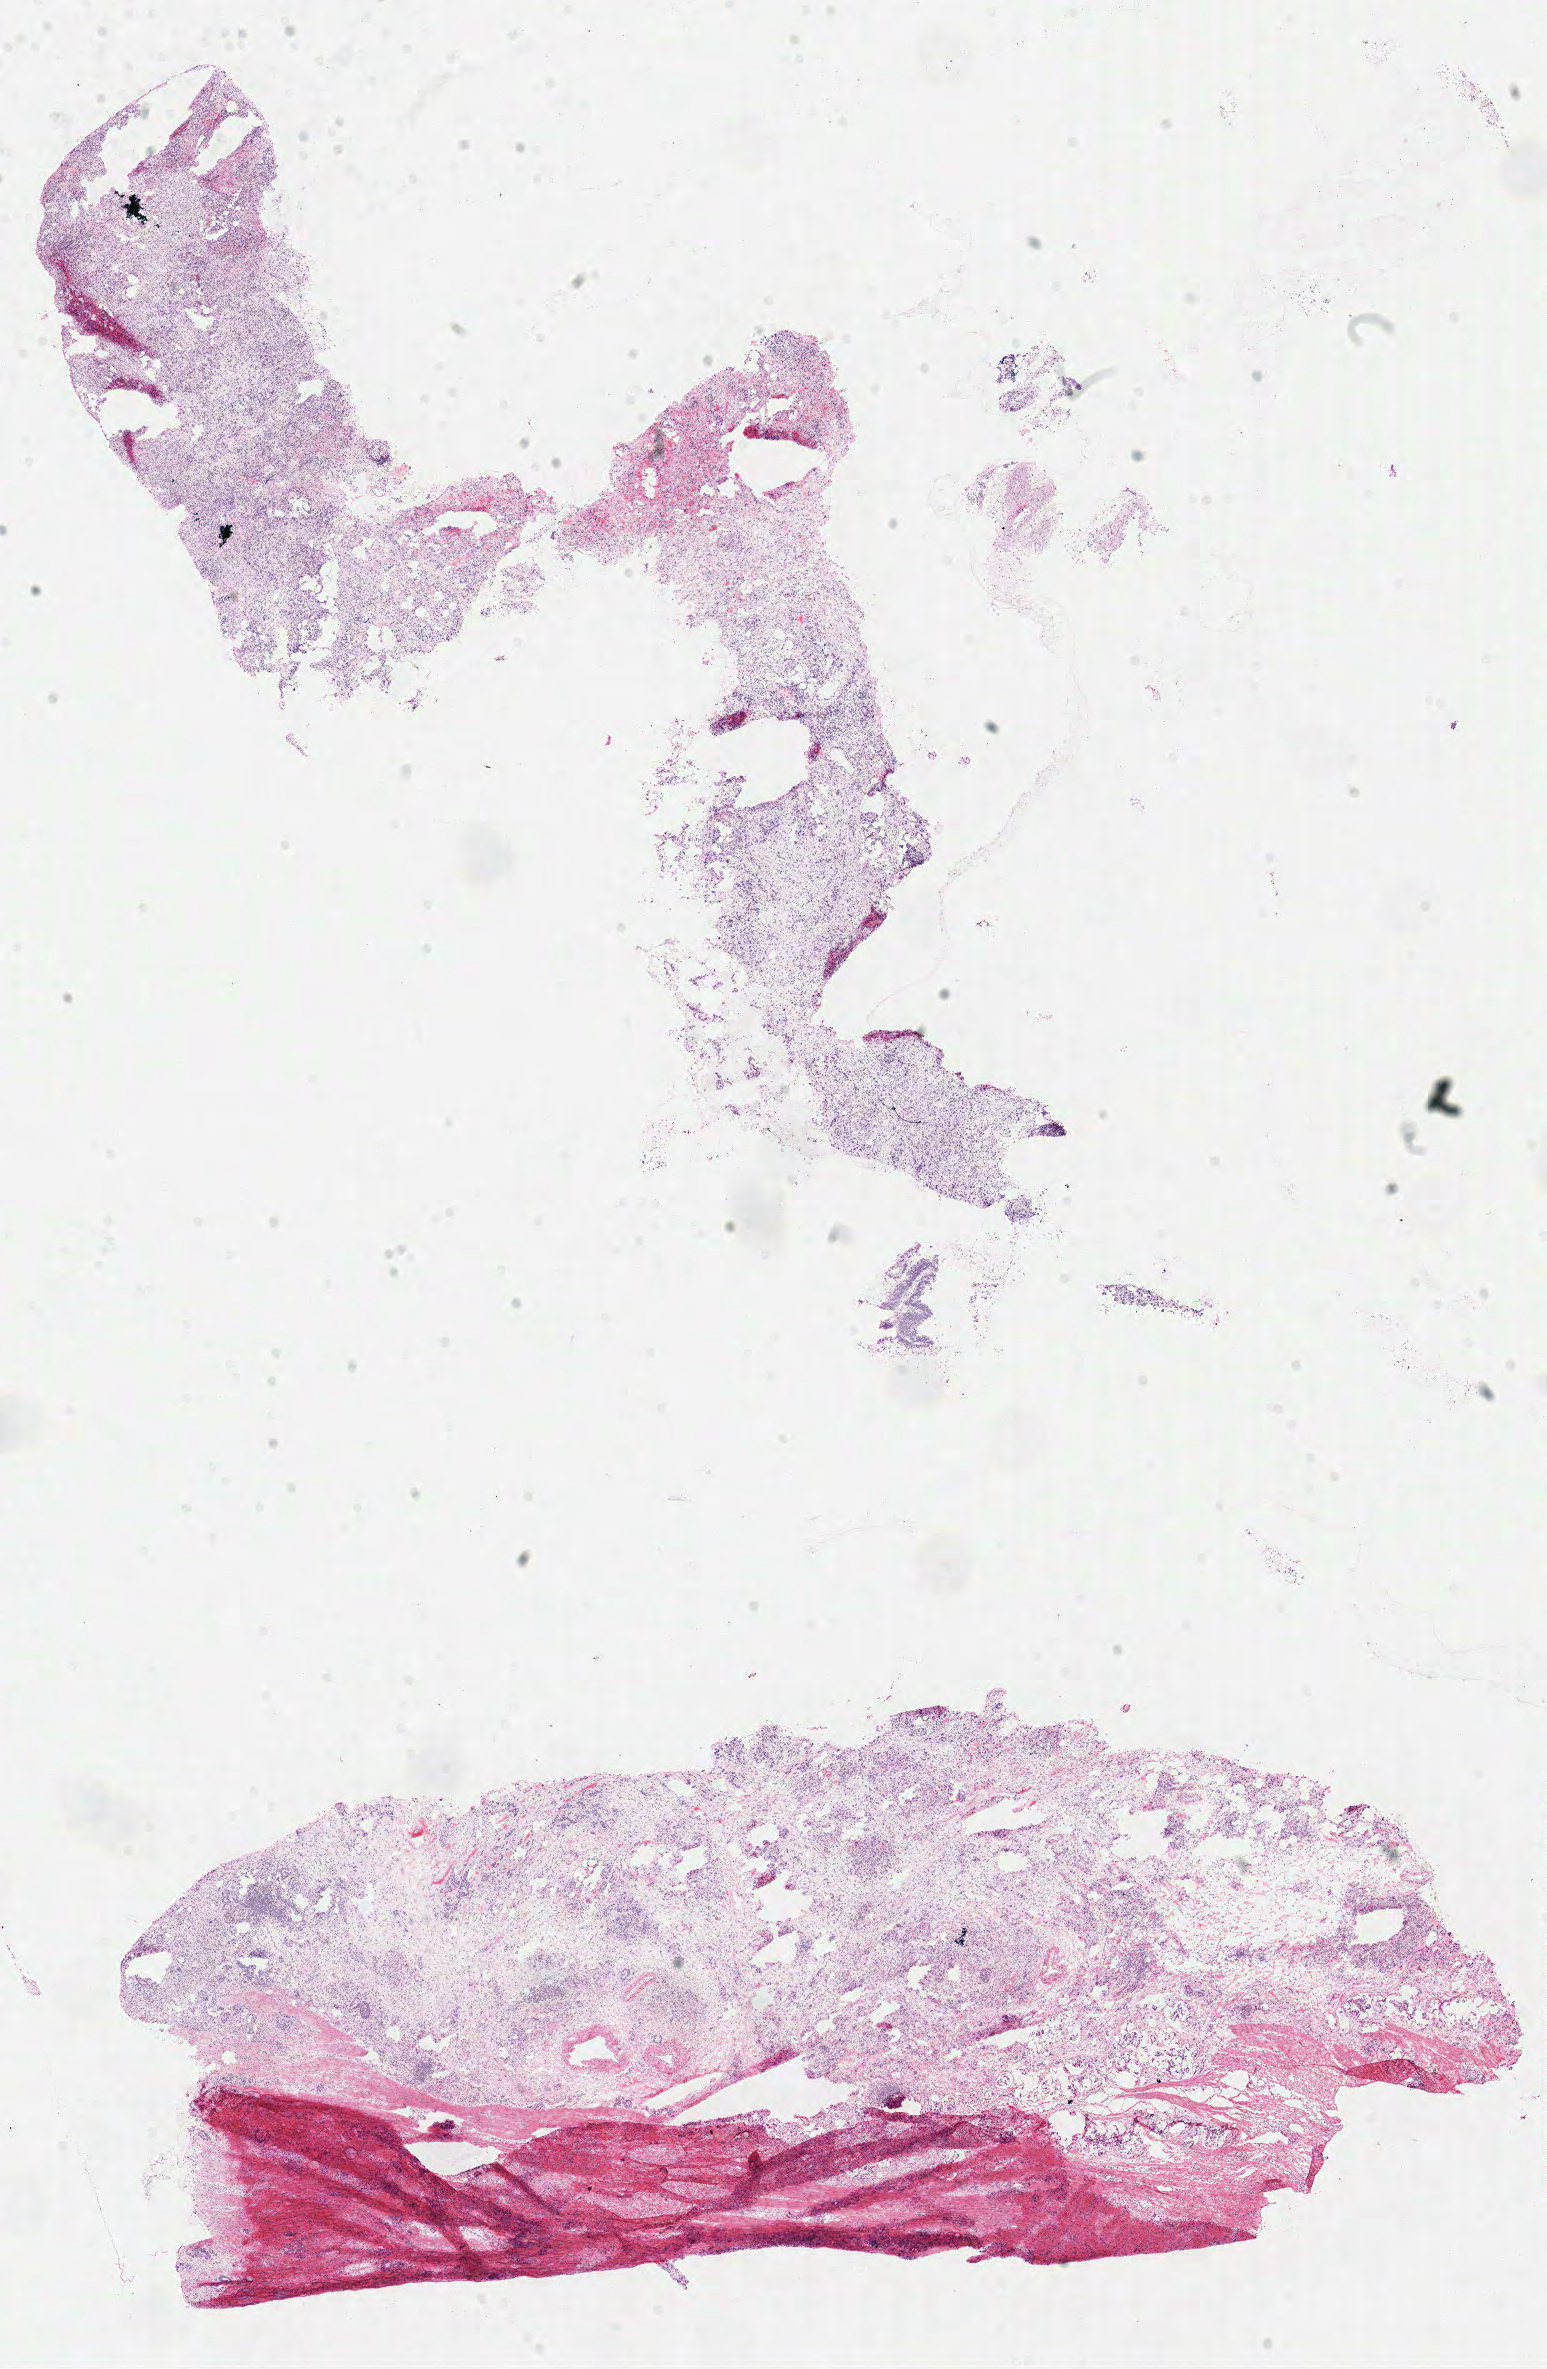
Digitized Hematoxylin and eosin (H&E) stained tissue section (whole slide), a low-resolution overview of the entire scanned area, about 12.2 x 18.7 mm. Frozen section. Colon, primary tumour sample. Female patient; age at initial diagnosis 57 years. Pathologist review of this section (percent, as recorded): tumour cells 80%, tumour nuclei 75%, normal cells 0%, stromal cells 20%, necrosis 0%.
- lymph nodes positive (case pathology): 11 of 40 examined
- AJCC pathologic stage: IIIC (7th edition)
- diagnosis: Adenocarcinoma, NOS (cecum)